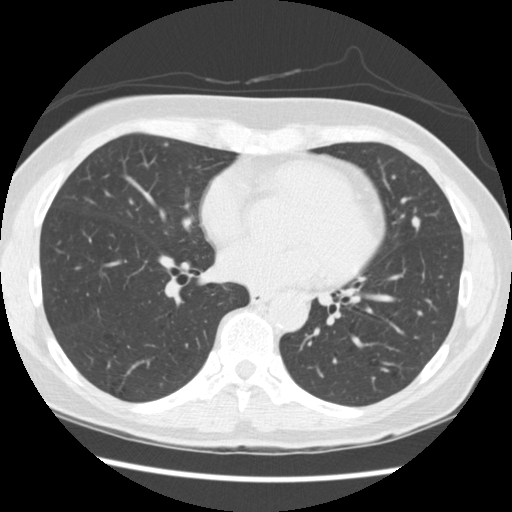
Low-dose screening chest CT, one axial slice; slice 122 of 262 in the series (ordered by position); reconstruction kernel STANDARD; 120 kVp; lung window (W 1500 / L -600 HU); 2.5 mm slice thickness; 512 × 512 image matrix.
Structures marked on this image (outlined manually by an expert reader):
- lesion 2 (tumor, lingular bronchus): bounding box (x1, y1, x2, y2) in pixels: (412, 216, 421, 228)